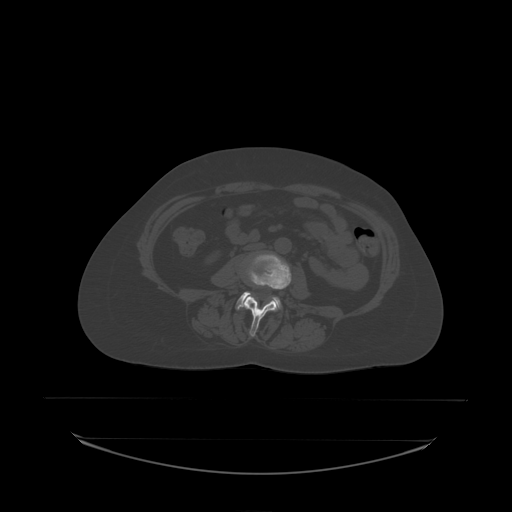
CT including the spine, one axial slice; slice 57 of 242 in the series (ordered by position); bone window (W 1800 / L 400 HU); 512 × 512 image matrix, field of view 500 × 500 mm. Female patient, age 53 years. Case-level facts recorded for this patient, not image findings: primary cancer: lung.
Structures marked on this image (semi-automatically segmented with operator editing):
- L3 vertebra: bounding box [x1, y1, x2, y2] px = [244, 254, 292, 338]
- L4 vertebra: [236, 292, 282, 310]